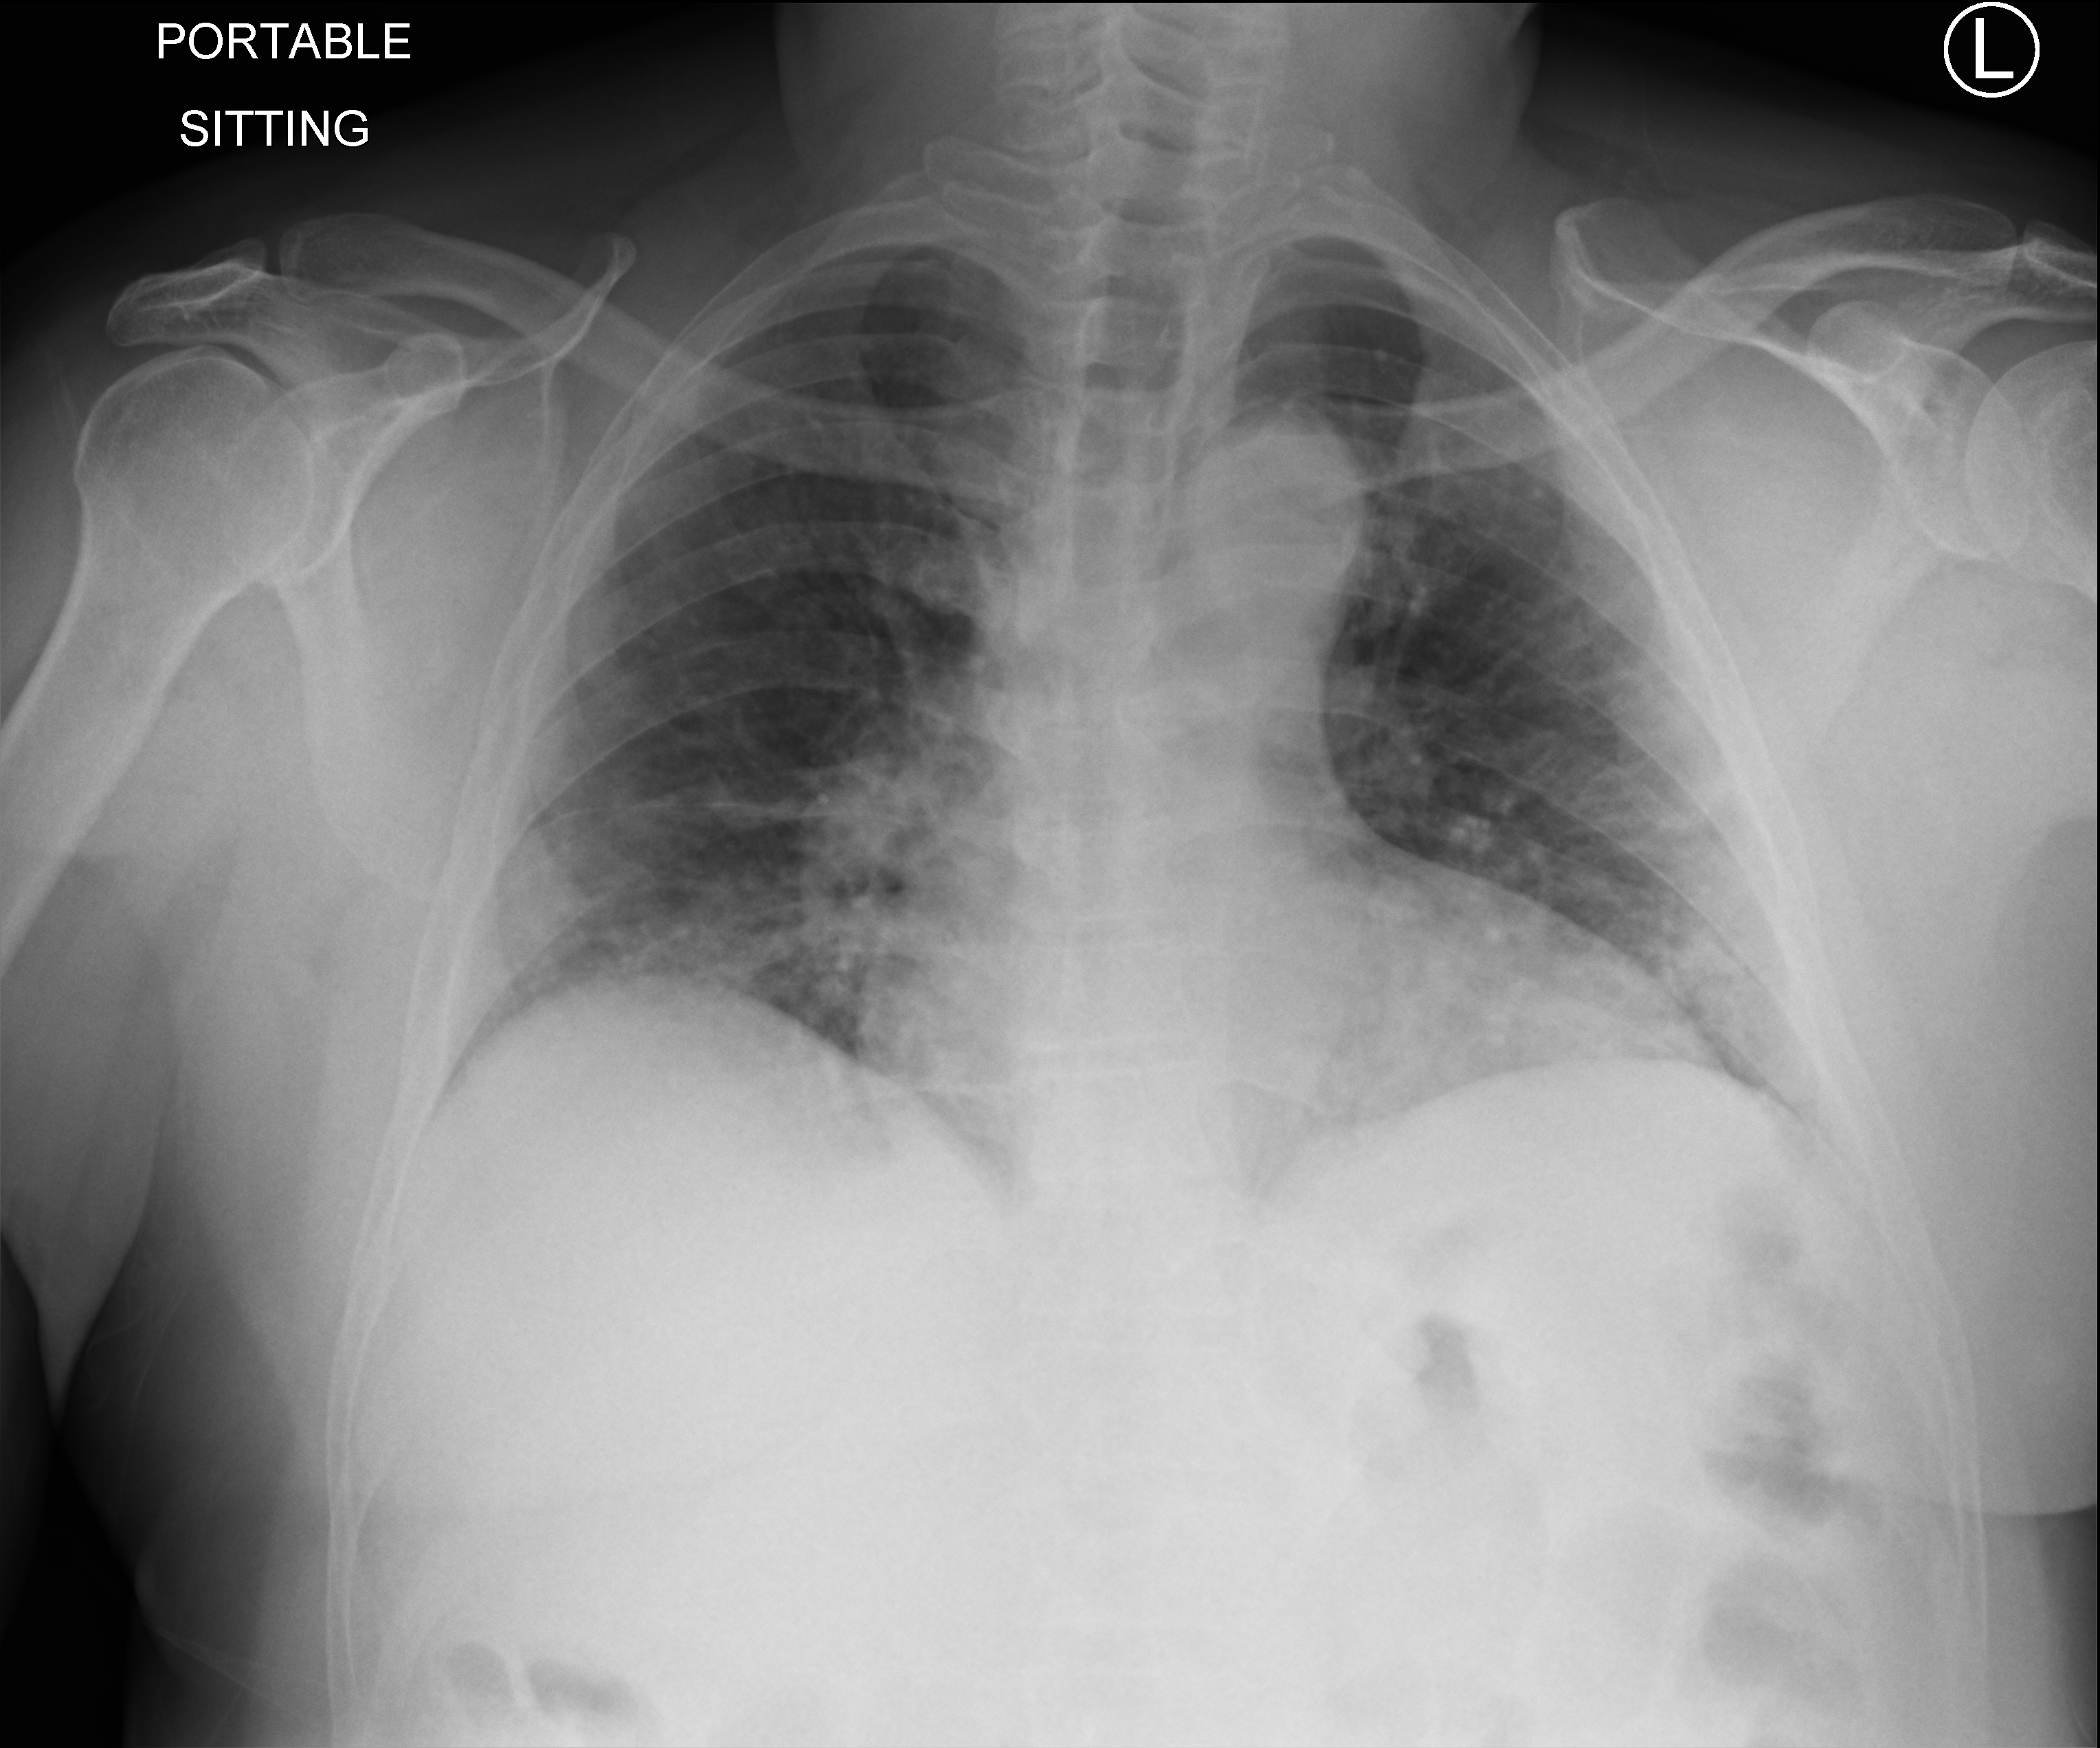
Portable chest radiograph, anteroposterior (AP) projection. Male patient hospitalised with COVID-19, age 18–59 years.
Hospital-stay facts (about this admission, not read from this image; timing relative to this image not recorded):
- COPD (admission record): no